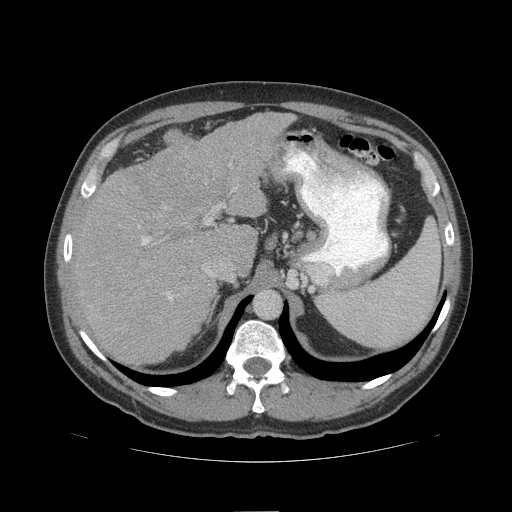
Contrast-enhanced abdominal CT (liver protocol), one axial slice. Slice 71 of 109 in the series (ordered by position). Reconstruction kernel STANDARD. 140 kVp. Soft-tissue window (W 400 / L 40 HU). 2.5 mm slice thickness. 512 × 512 image matrix, field of view 420 × 420 mm. Case-level facts recorded for this patient, not image findings: diagnosis: hepatocellular carcinoma (patient treated with transarterial chemoembolisation; whether this scan precedes or follows treatment is not stated here); TNM stage (as recorded): Stage-IIIB; Child-Pugh class: A; tumour differentiation: poorly differentiated; tumour nodularity: multinodular.
Structures marked on this image (semi-automatically segmented with operator editing):
- liver parenchyma outside the tumour (the mass and vessels are separate outlines, so this box may not span the whole liver): bounding box <72,112,295,364> (left, top, right, bottom; pixels)
- mass: <124,150,226,219>
- liver vessels: <142,218,211,300>